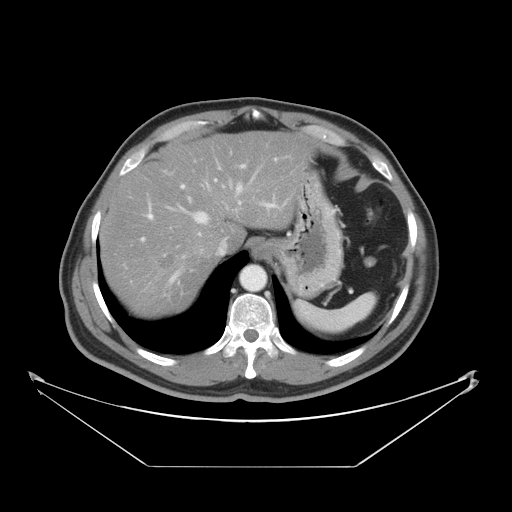
Contrast-enhanced abdominal CT, one axial slice; position 35 of 46 along the scan axis; intravenous contrast given; soft-tissue window (W 400 / L 40 HU); 512 × 512 image matrix. Male patient, age 57 years. Case-level facts recorded for this patient, not image findings: diagnosis: colorectal cancer liver metastases, imaged before liver resection; multiple liver metastases: no; largest metastasis: 3.3 cm; disease in both lobes: no.
Structures marked on this image (expert manual segmentation):
- hepatic veins: box from (x=181, y=186) to (x=241, y=223) px
- liver: (x=101, y=134)–(x=305, y=316)
- planned liver remnant (the part of the liver to remain after resection): (x=101, y=134)–(x=305, y=313)
- portal vein (with intrahepatic branches): (x=140, y=165)–(x=245, y=286)
- liver metastasis: (x=155, y=250)–(x=178, y=272)